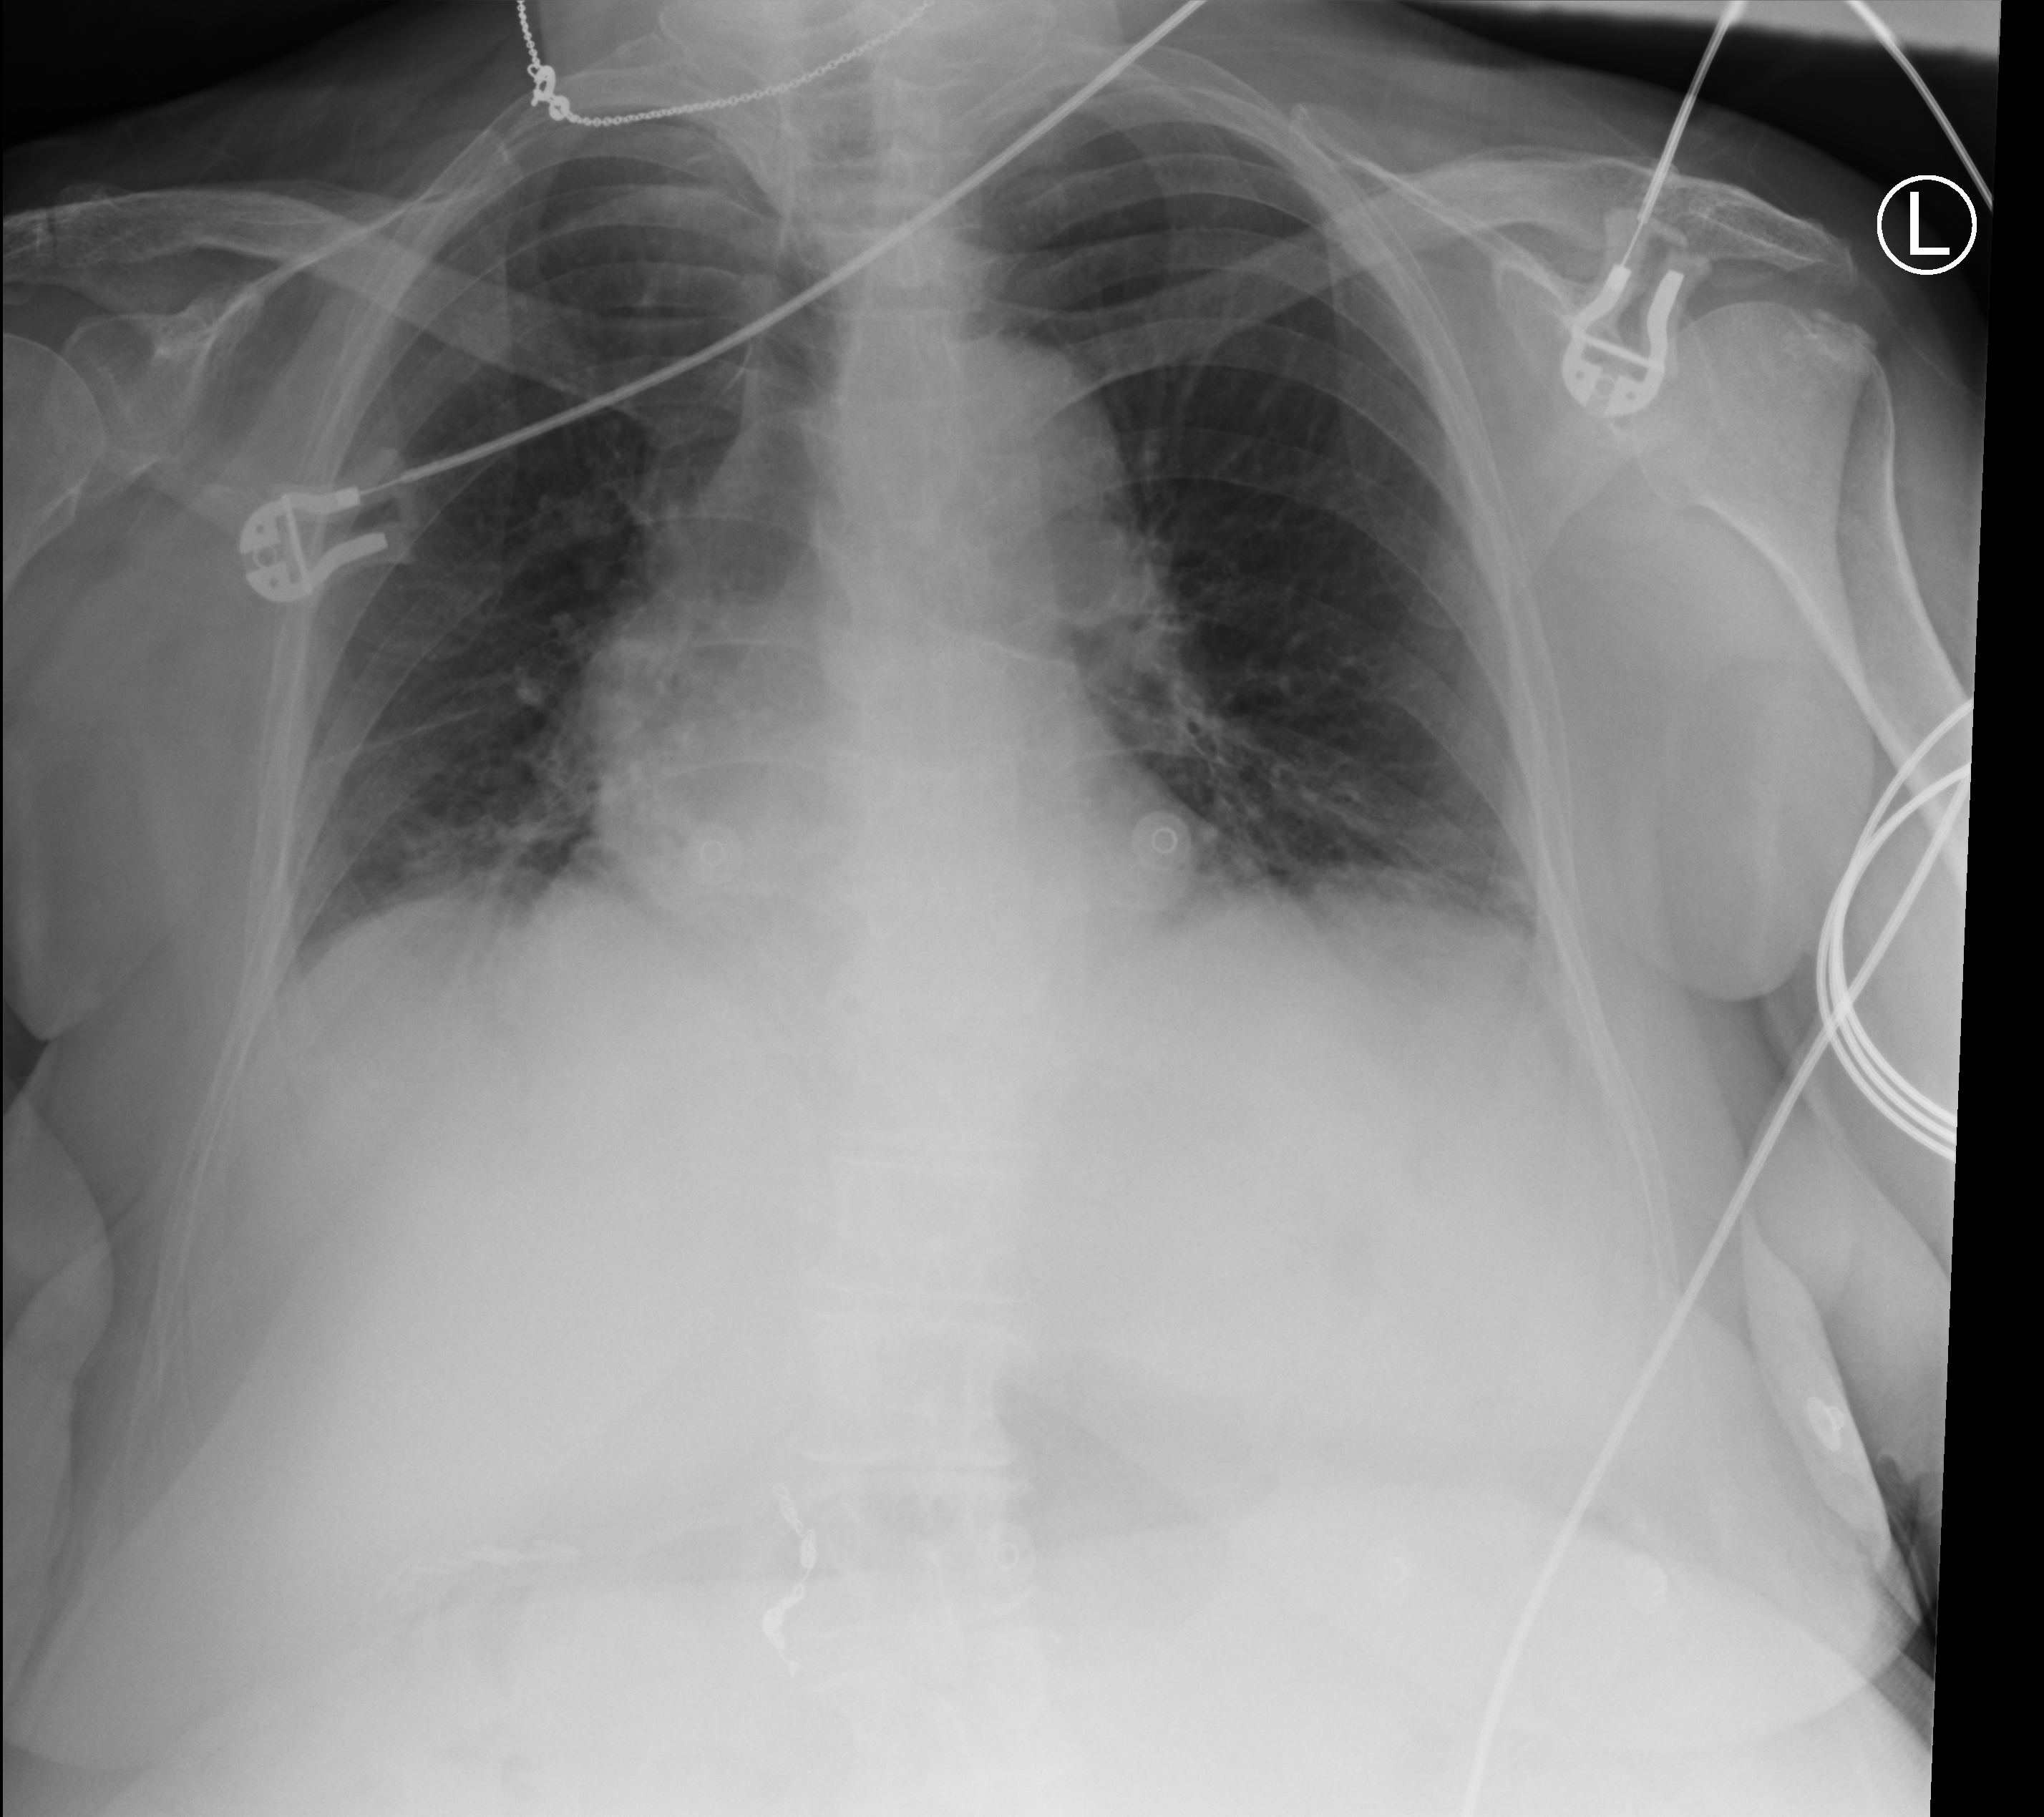
Chest X-ray (portable), anteroposterior (AP) projection. Patient hospitalised with COVID-19; female, aged 75–90 years.
Admission-level facts for this patient (not findings on this image; timing relative to this image not recorded): COPD (admission record): no; mechanically ventilated during this hospital stay: no.